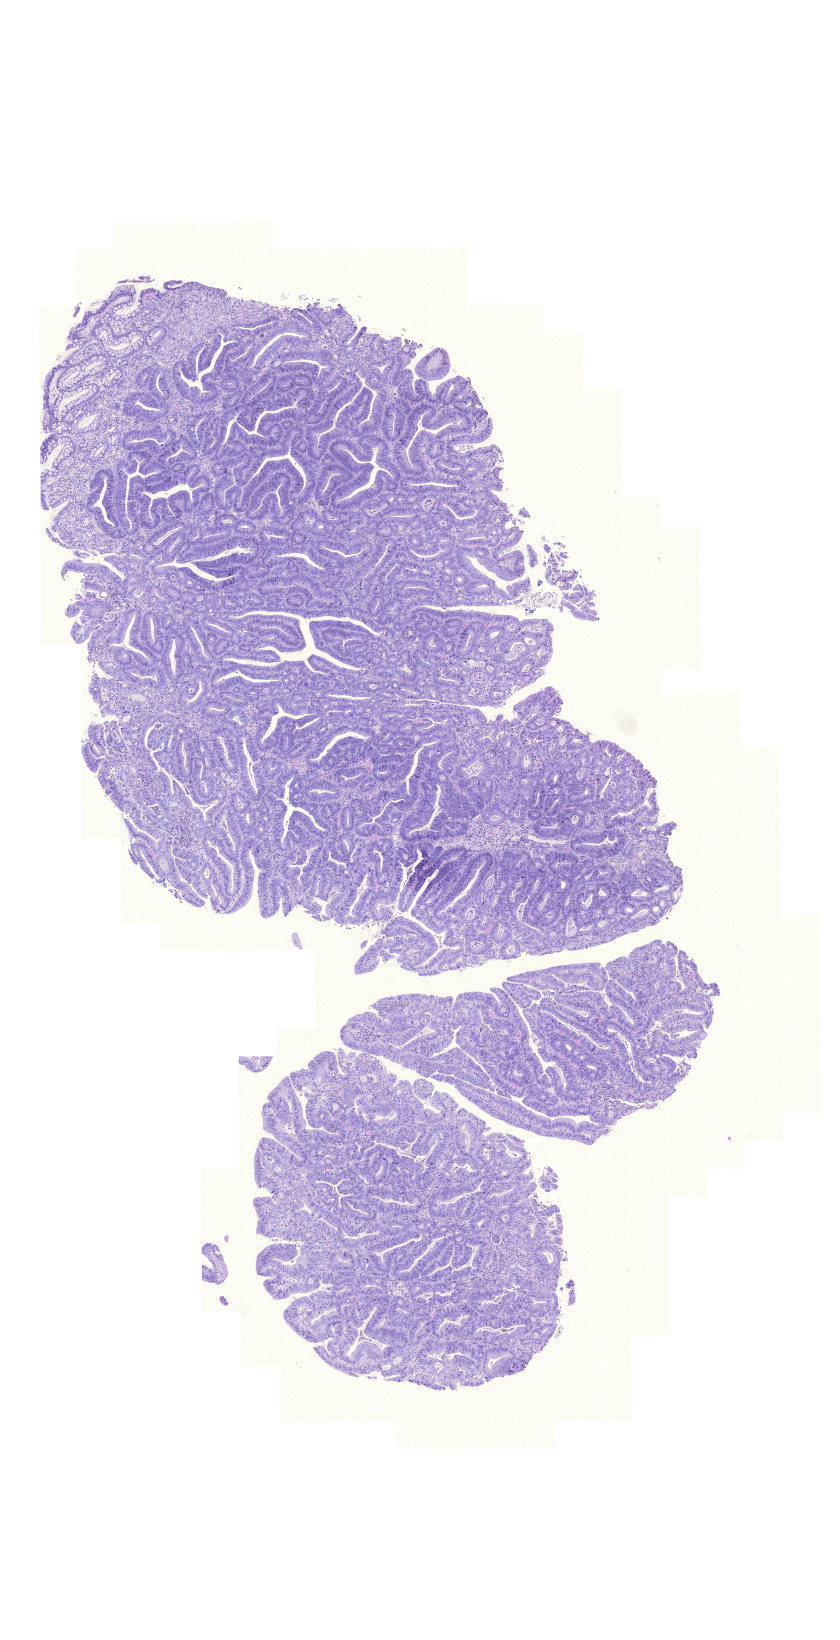
Whole-slide histology image, H&E-stained — a low-resolution overview of the entire scanned area, about 6.2 x 12.2 mm (acquisition: 20x scan). FFPE section. Primary tumour sample from the colon. Patient: male, age at initial diagnosis 72 years.
AJCC pathologic stage: IIIB (6th edition). TNM: T3 N1 M0. Lymph nodes positive (case pathology): 2 of 30 examined. Histologic diagnosis: Adenocarcinoma, NOS (sigmoid colon).